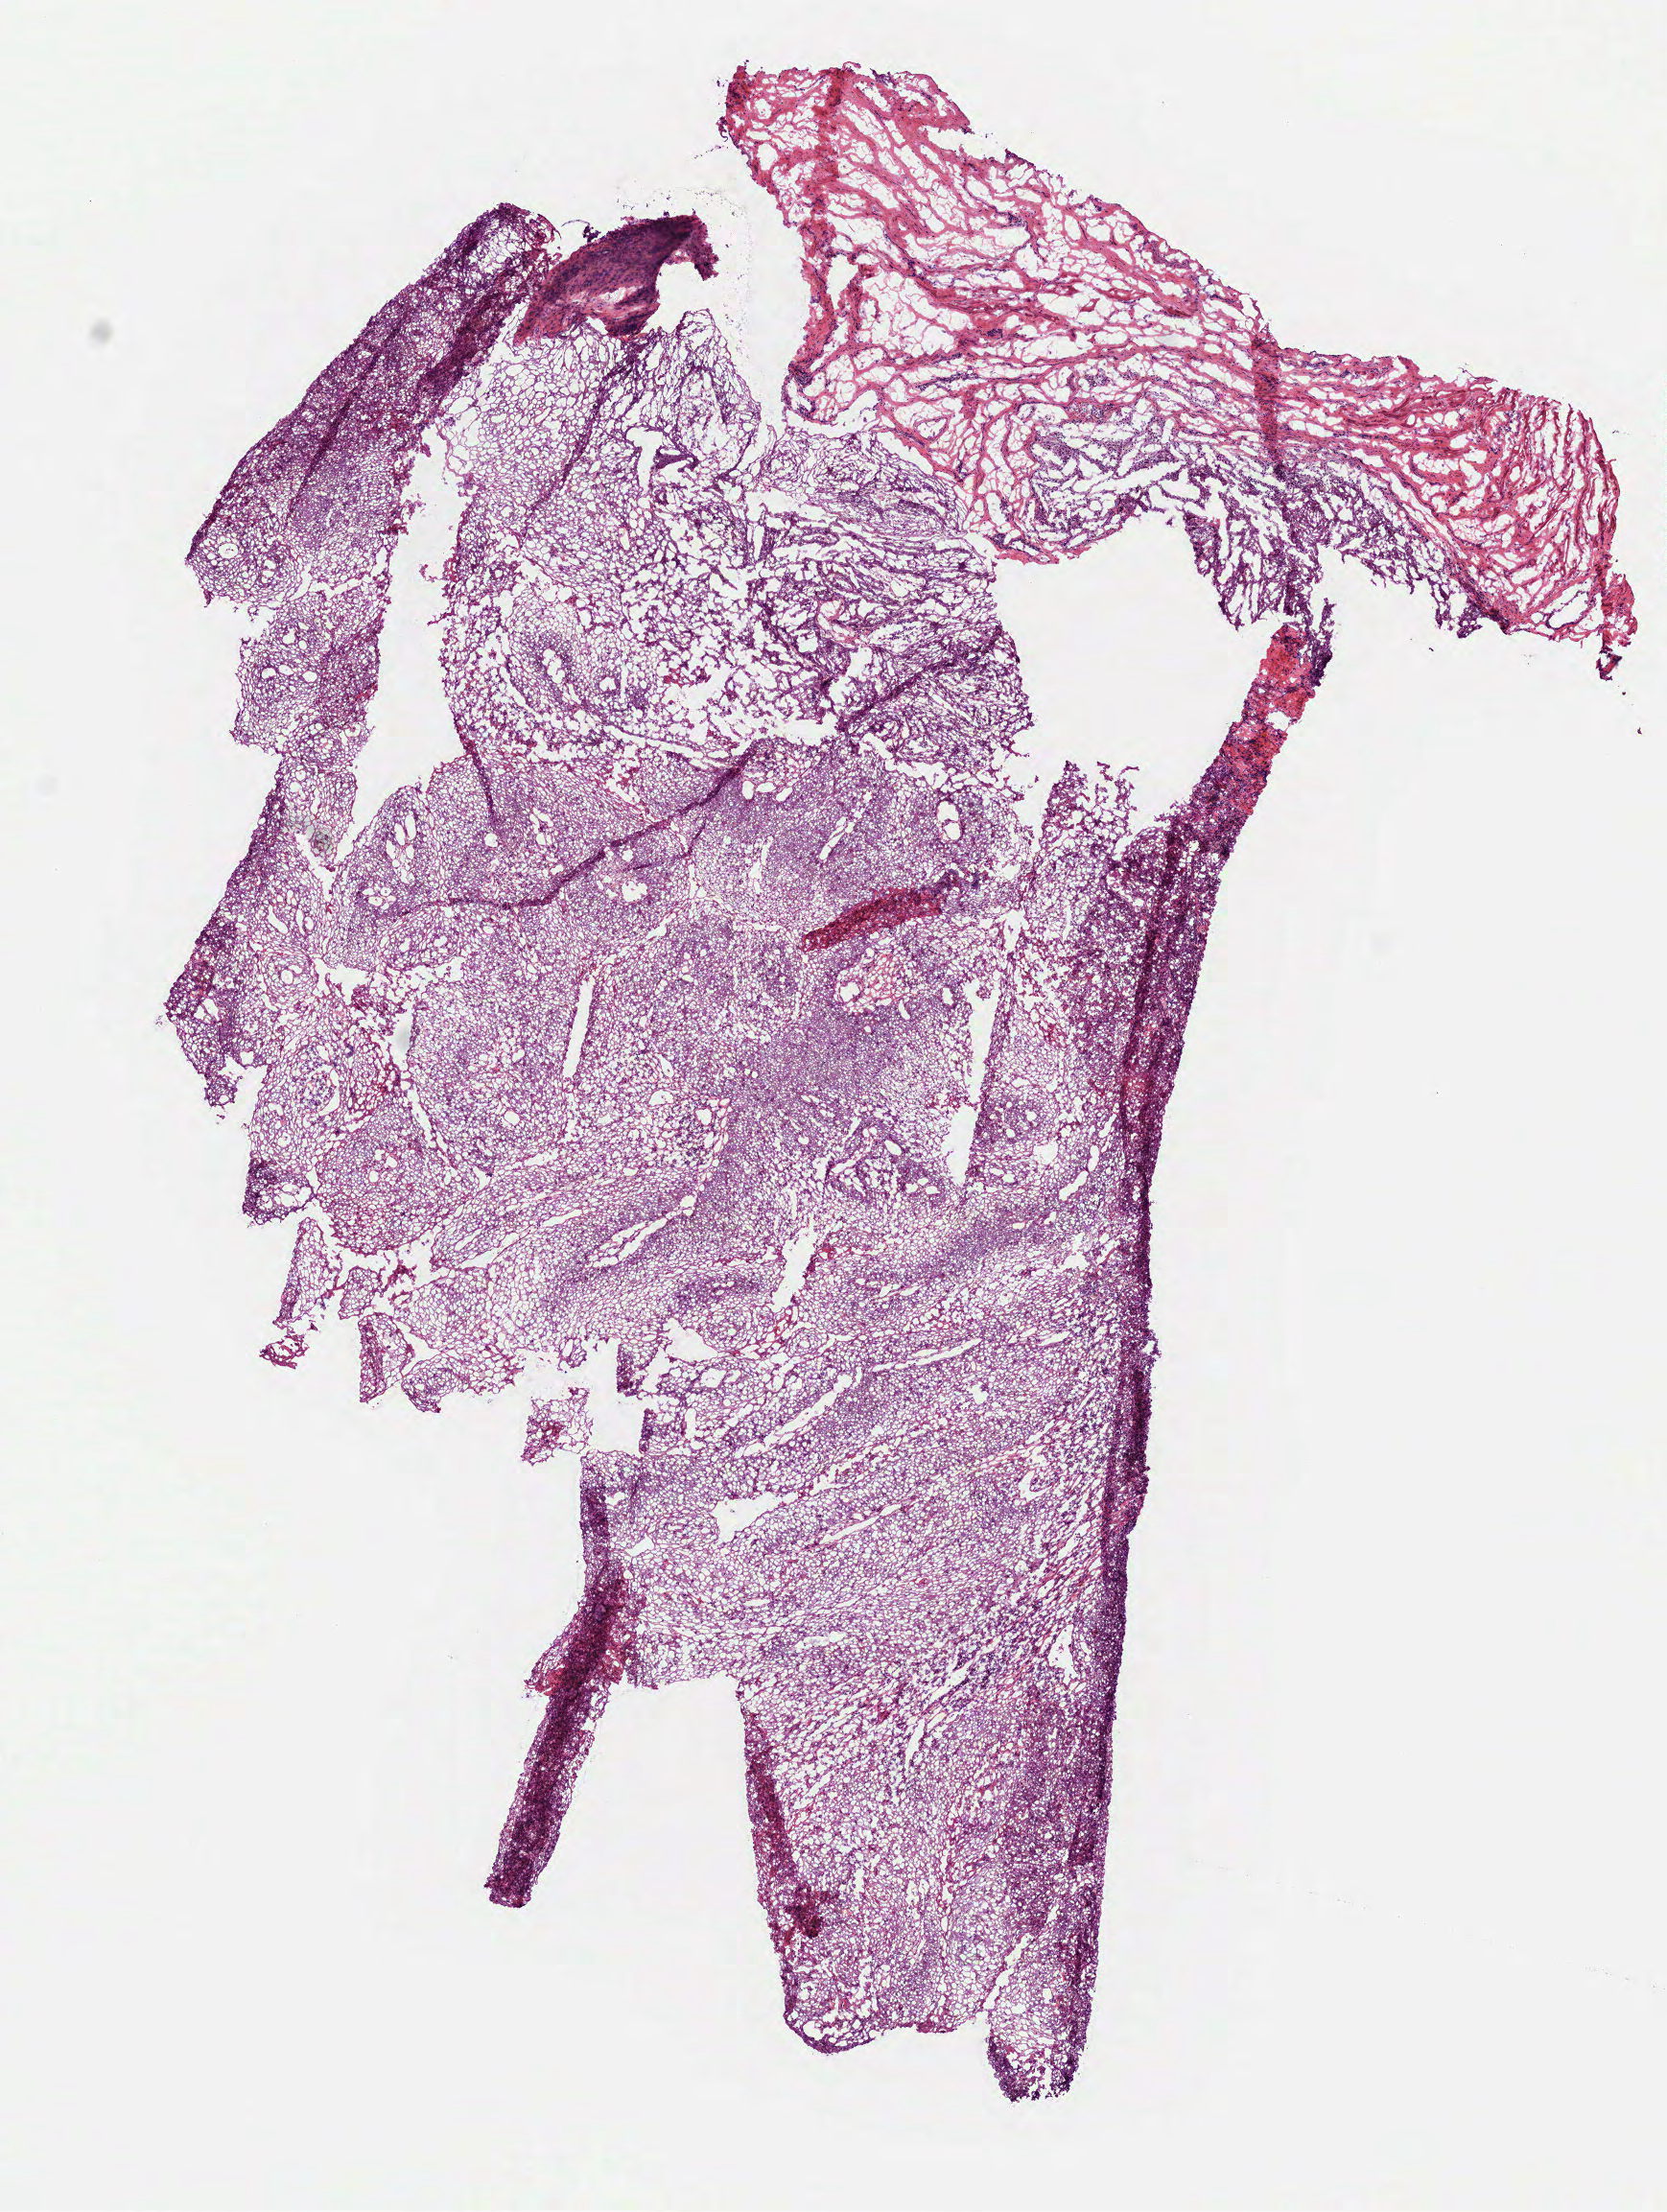
Whole-slide histology image, Hematoxylin and eosin (H&E) stained — a low-resolution overview of the entire scanned area, about 7.0 x 9.3 mm (acquisition: 40x scan), frozen section from the bottom of the tissue portion, sample: primary tumour, head and neck. Male patient; age at initial diagnosis 64 years. Histologic grade: G1 (well differentiated). Pathologist review of this section (percent, as recorded): tumour cells 90%, tumour nuclei 80%, normal cells 0%, stromal cells 10%, necrosis 0%.
TNM: T4a N0. Diagnosis: Squamous cell carcinoma, NOS (larynx, NOS). AJCC pathologic stage: IVA (7th edition).